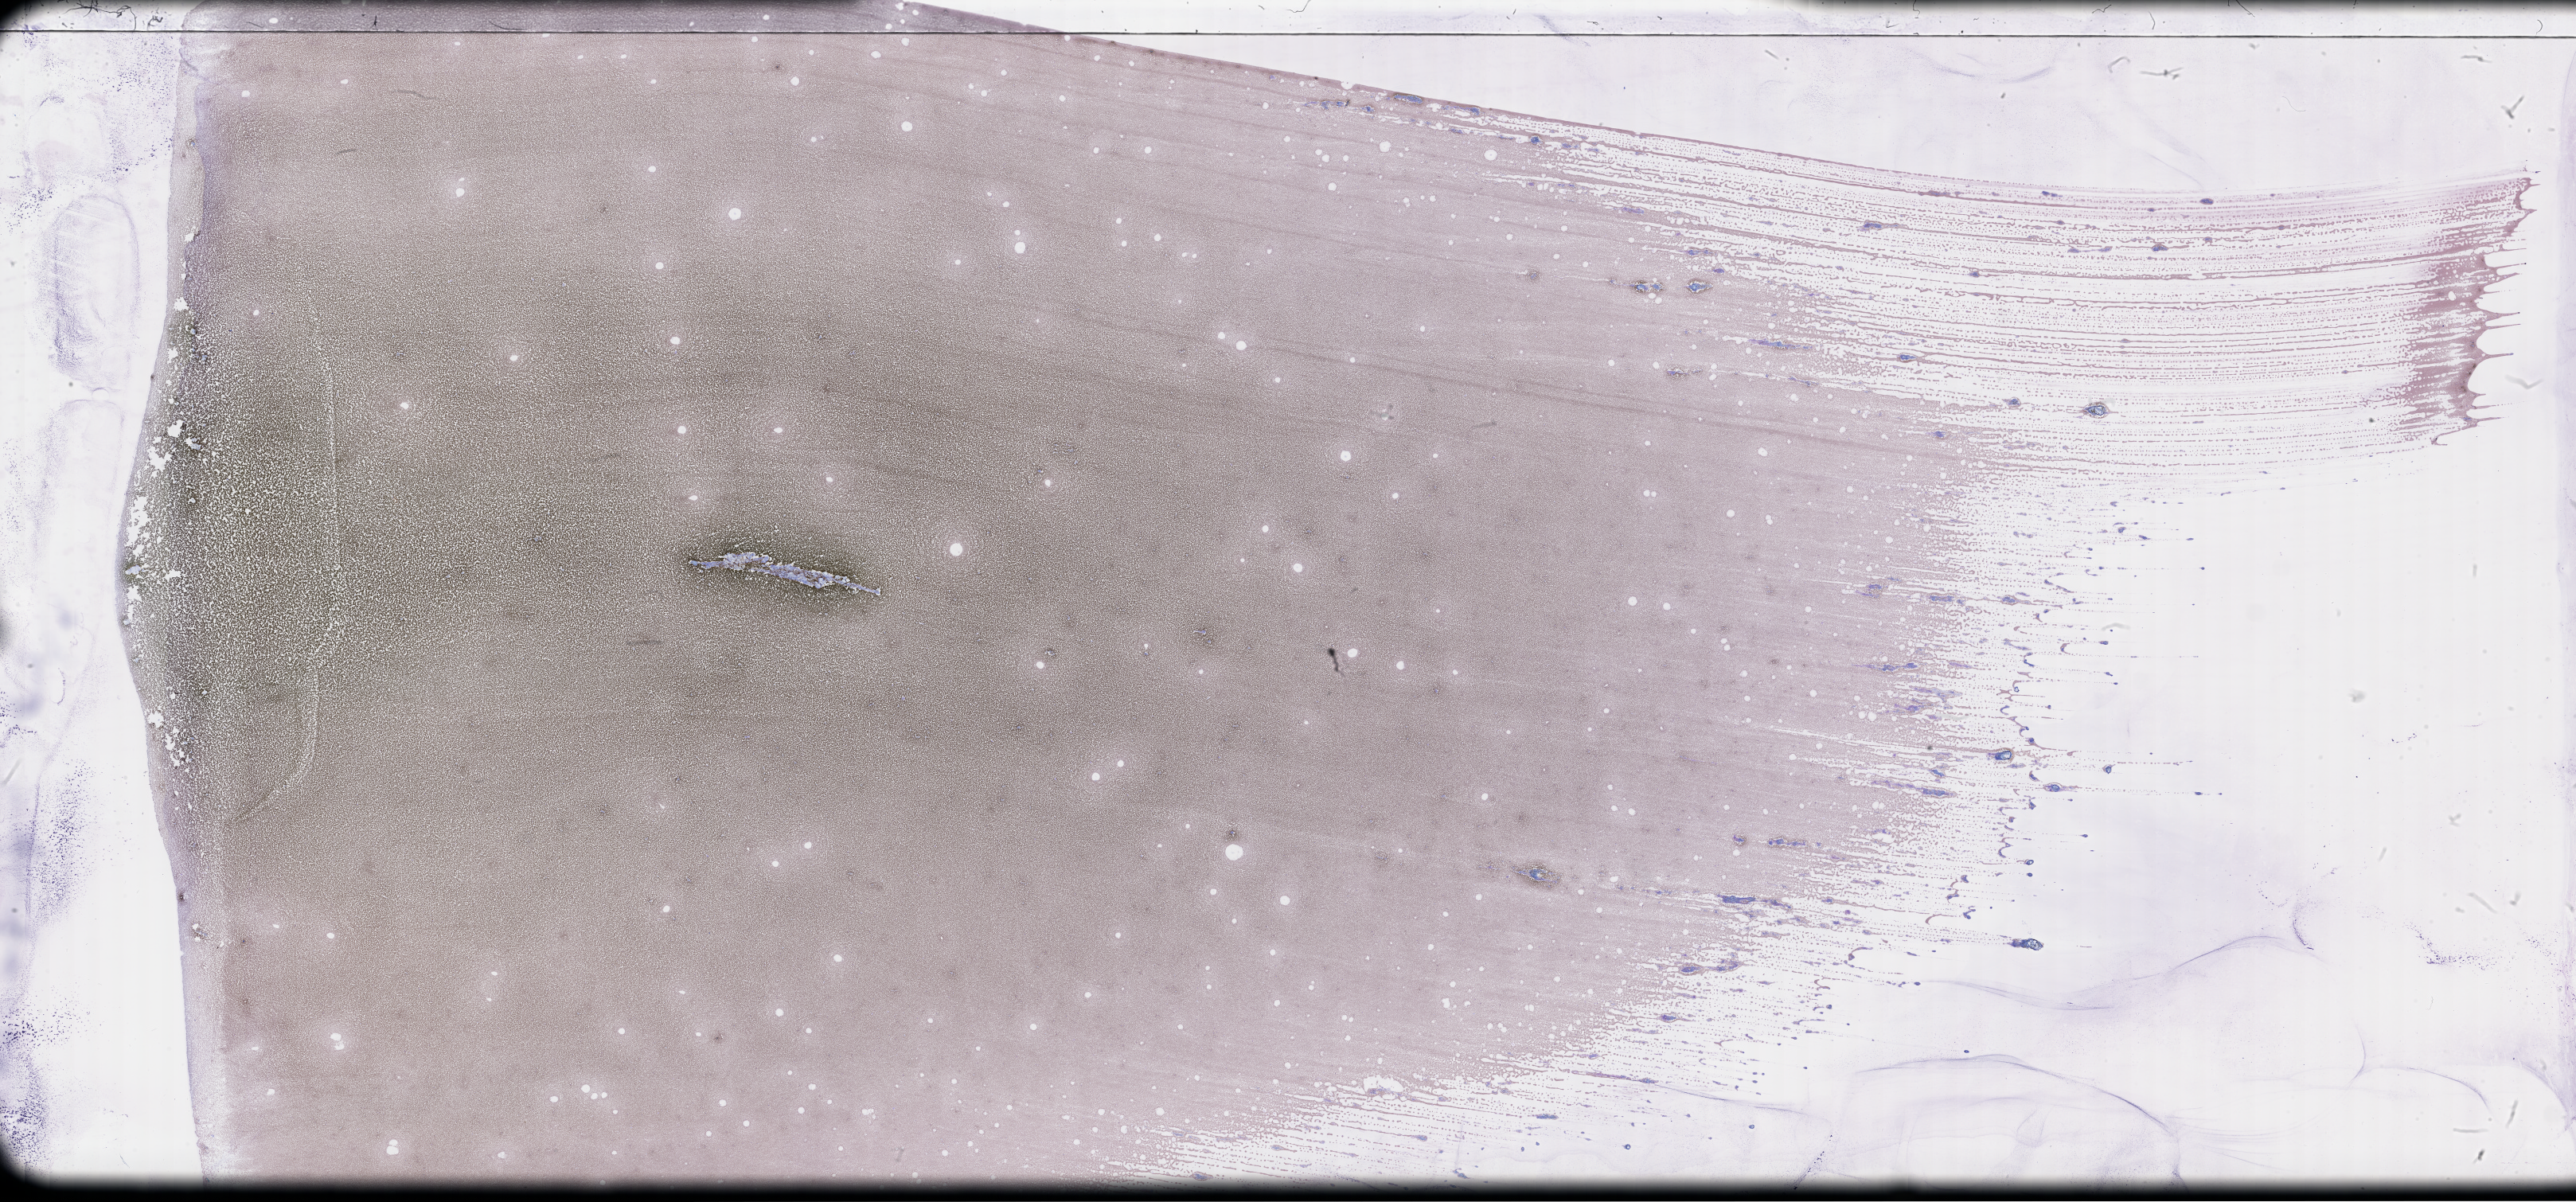
Whole-slide image of a whole blood smear, Wright-Giemsa stain — low-resolution overview of the scanned area, about 52.3 x 24.4 mm. Smear from an EDTA sample. Collected on treatment. Patient: female.
Patient diagnosis: Plasma Cell Myeloma.